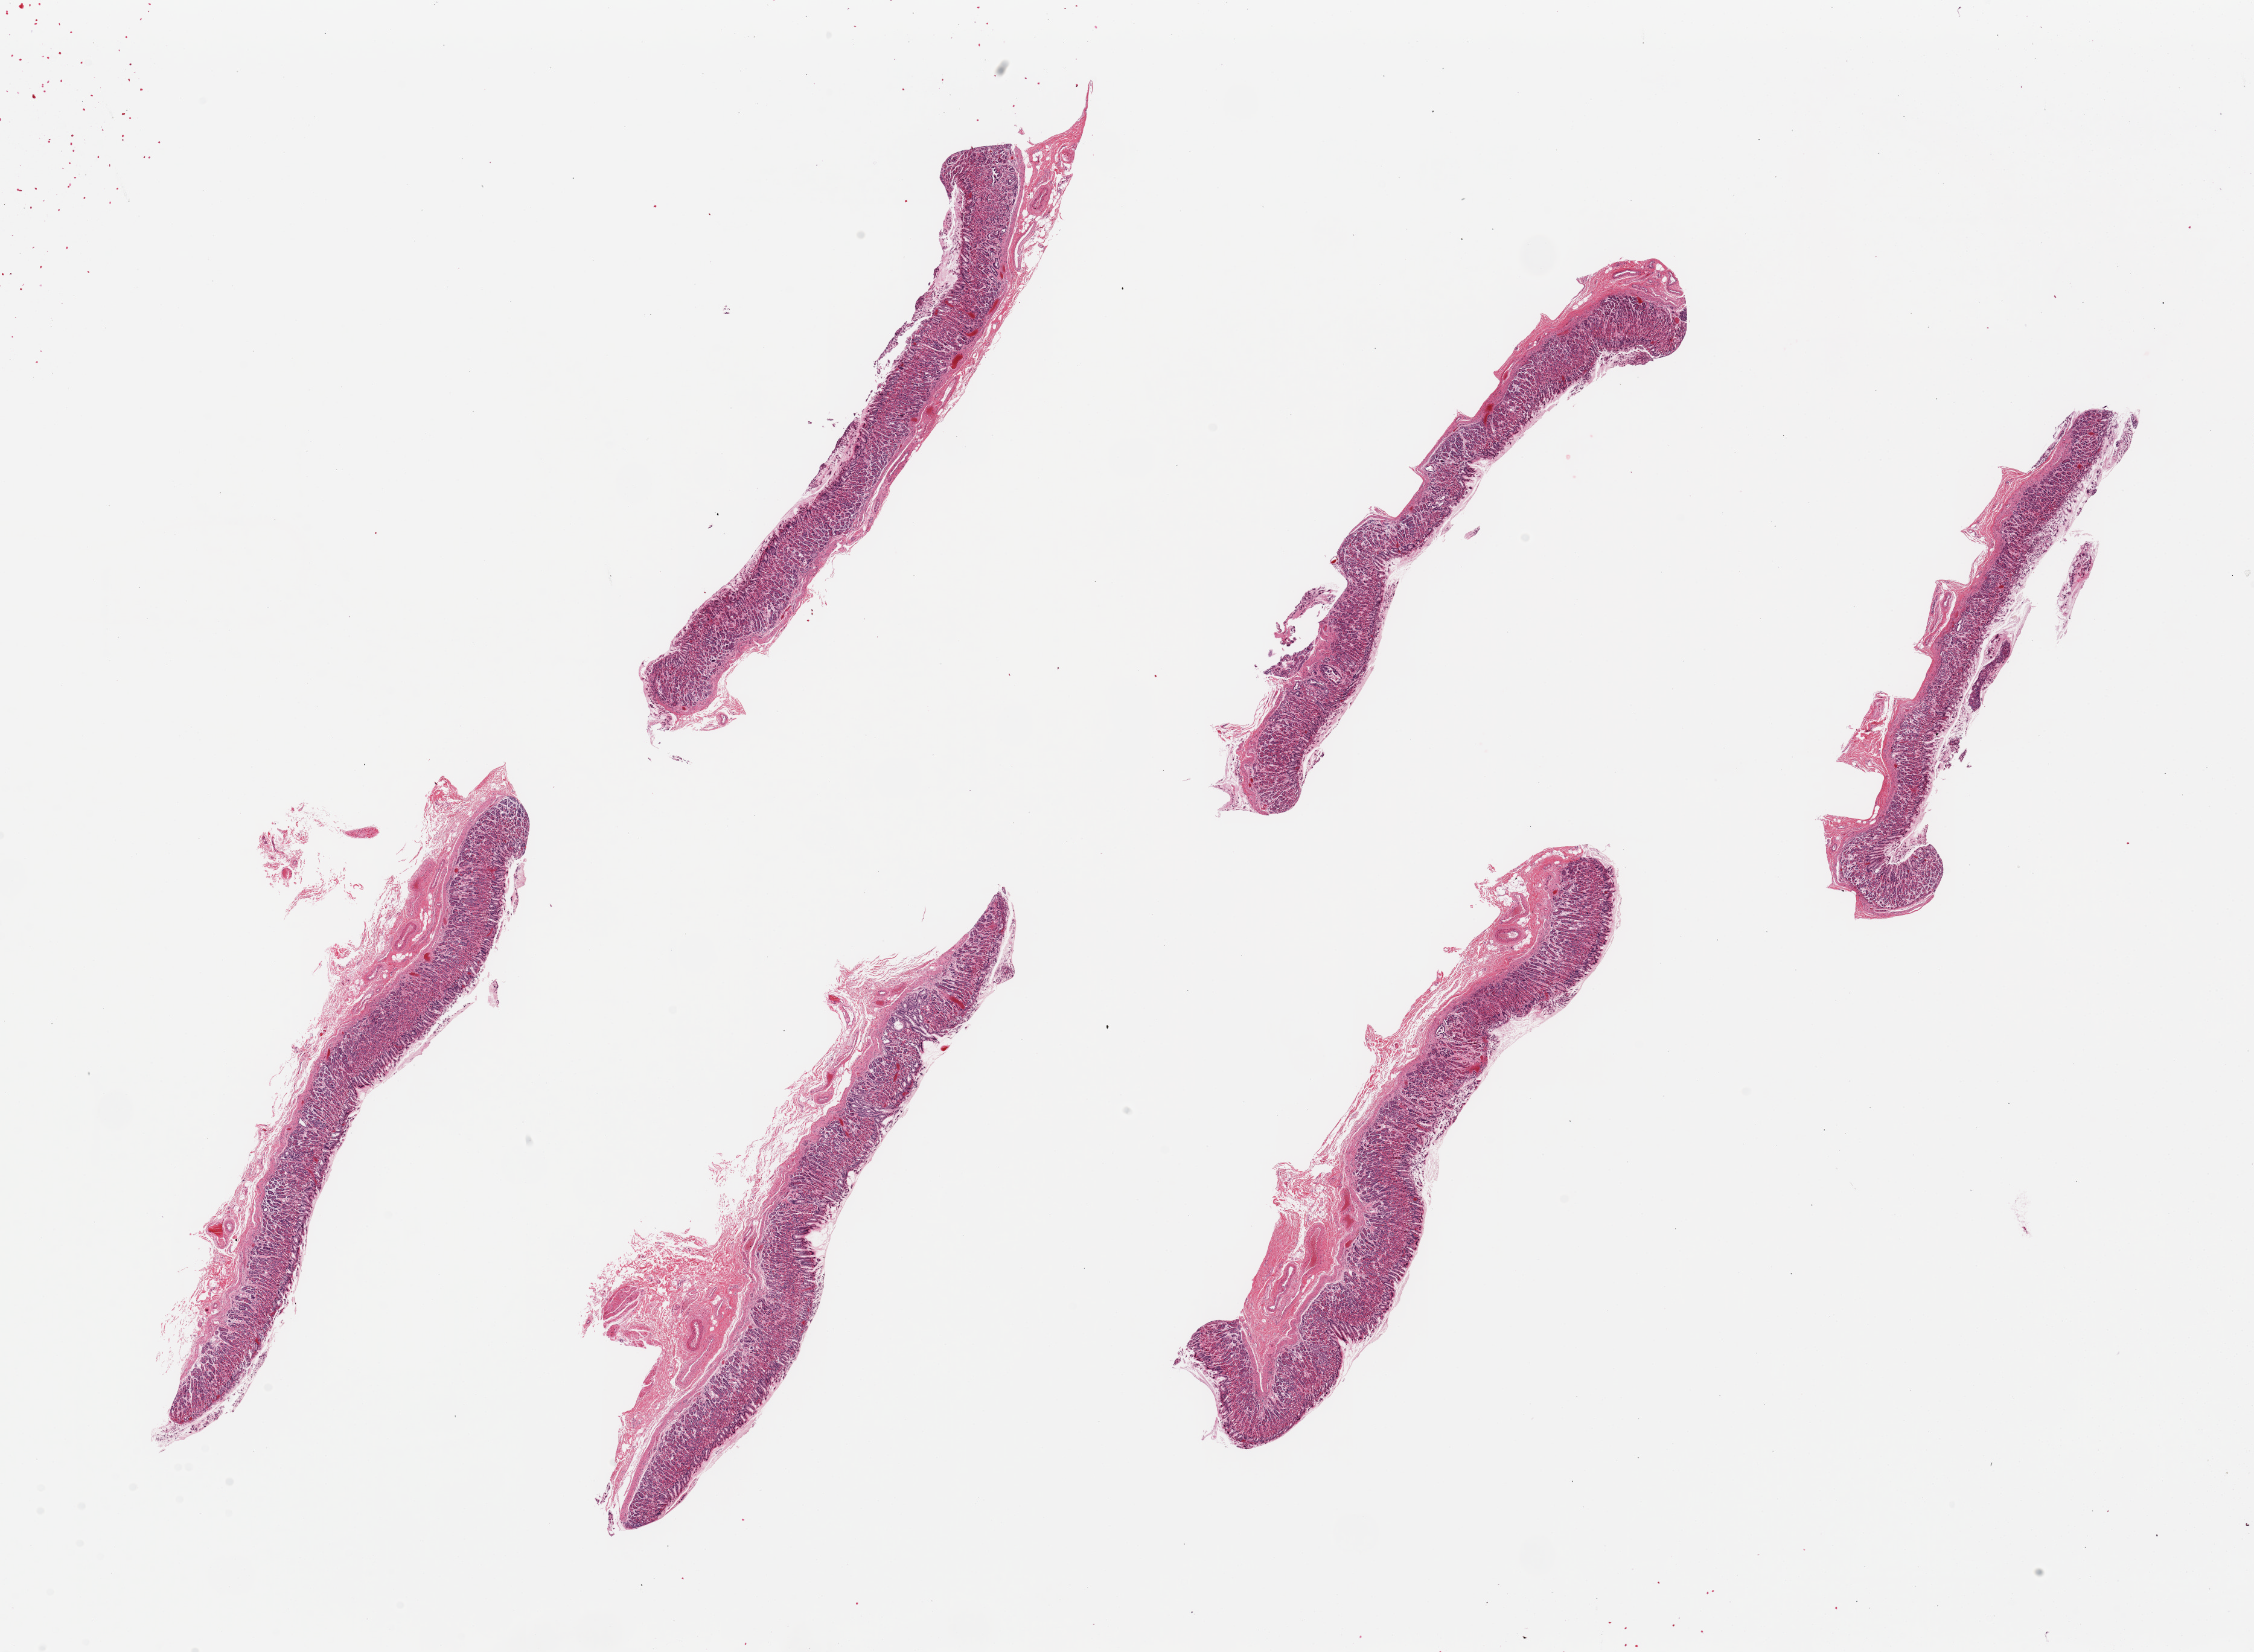
Haematoxylin and eosin whole-slide image, low-resolution overview of the scanned area, about 29.5 x 21.6 mm (acquisition: 20x scan), PAXgene-fixed, paraffin-embedded tissue, sampled site (target tissue): stomach, tissue donor sample. Donor sex: male.
Review note (as recorded): 6 pieces ~9x1mm, remarkaby well-preserved; mucosa is 70--95% of thickness.